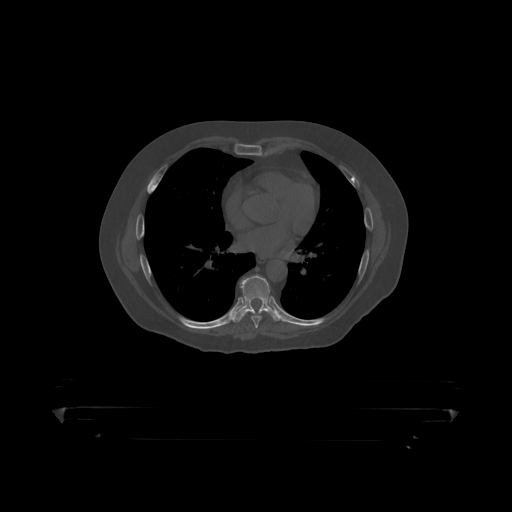
CT including the spine, one axial slice. Slice 266 of 390 in the series (ordered by position). Bone window (W 1800 / L 400 HU). 1.25 mm slice thickness. 512 × 512 image matrix, field of view 650 × 650 mm. Male patient, age 60 years. From the clinical record (not read from this slice): primary cancer: prostate.
Structures marked on this image (semi-automatically segmented with operator editing):
- T6 vertebra: bounding box [x1, y1, x2, y2] px = [245, 300, 251, 306]
- T7 vertebra: [251, 312, 263, 319]
- T8 vertebra: [232, 276, 277, 318]